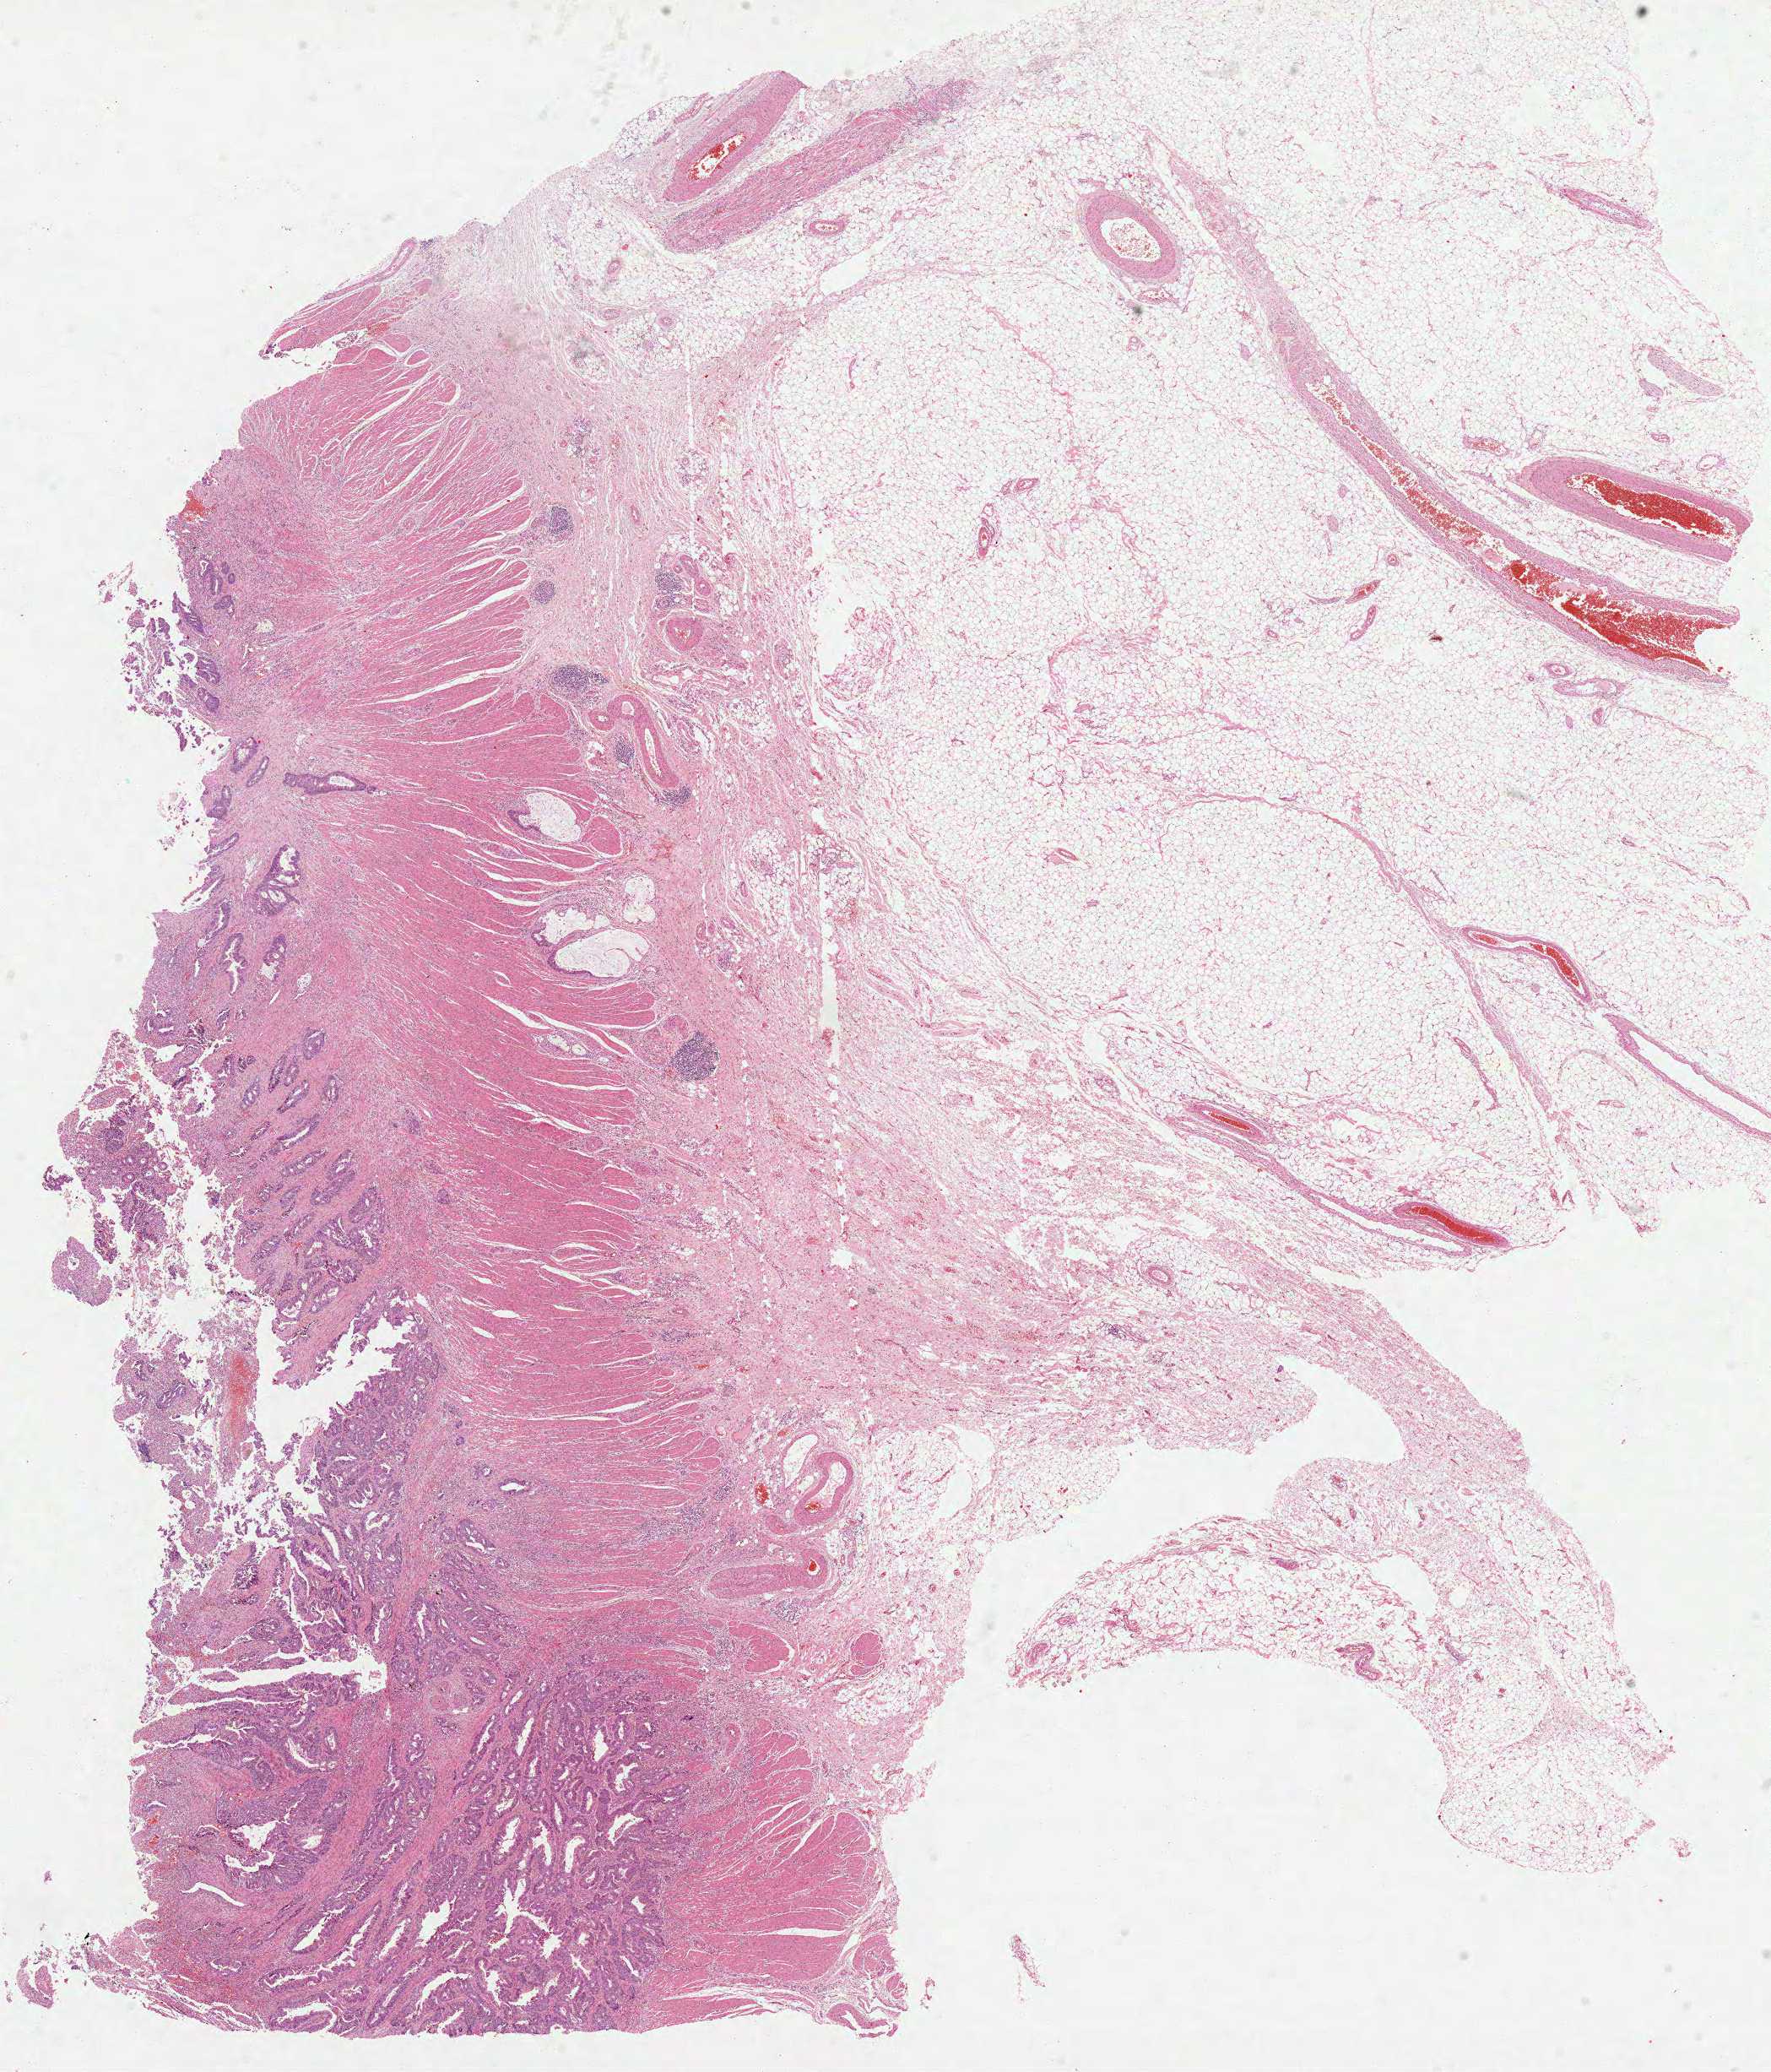
Whole-slide histology image, H&E, a low-resolution overview of the entire scanned area, about 16.9 x 19.8 mm. FFPE section. Primary tumour sample from the rectum. Patient: female, age at initial diagnosis 48 years.
Histologic diagnosis: Adenocarcinoma in tubulovillous adenoma.